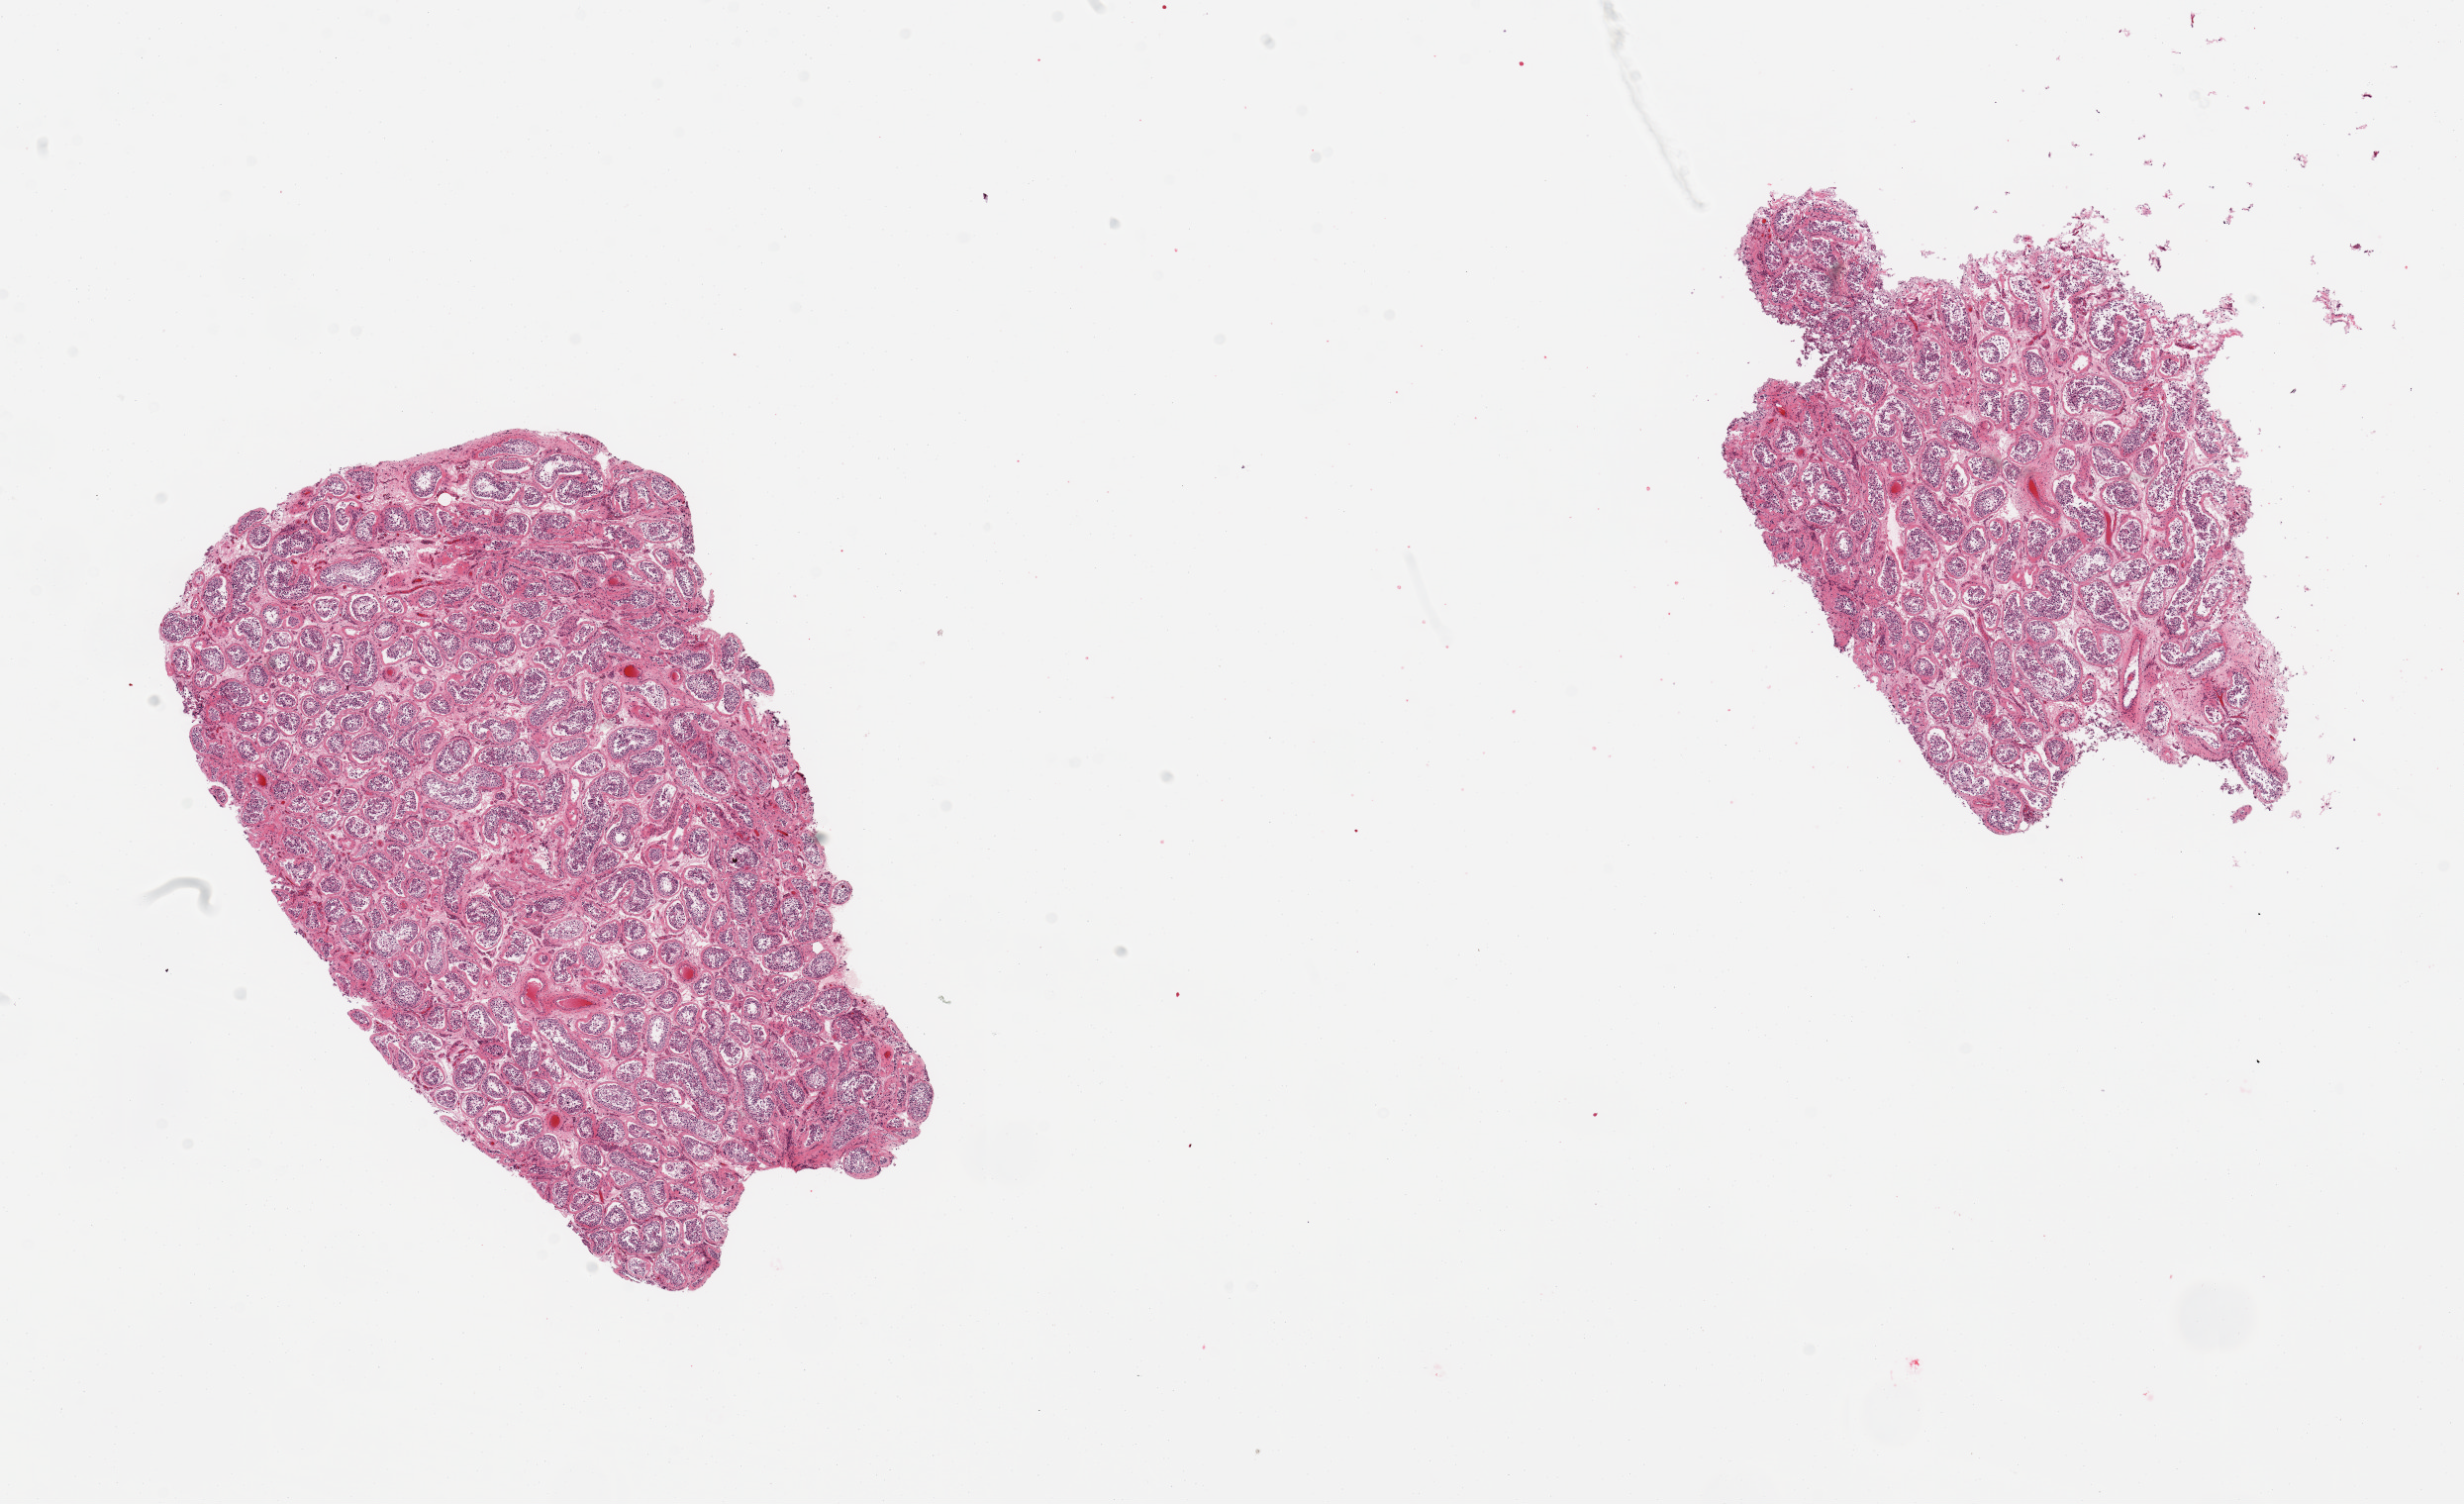
Digitized H&E-stained section, whole scanned area (about 19.7 x 12.0 mm) shown as a low-resolution overview. PAXgene-fixed, paraffin-embedded tissue. Sampled site (target tissue): testis. Tissue donor sample. Donor: male.
Pathologist's review note for this sample: 2 pieces.